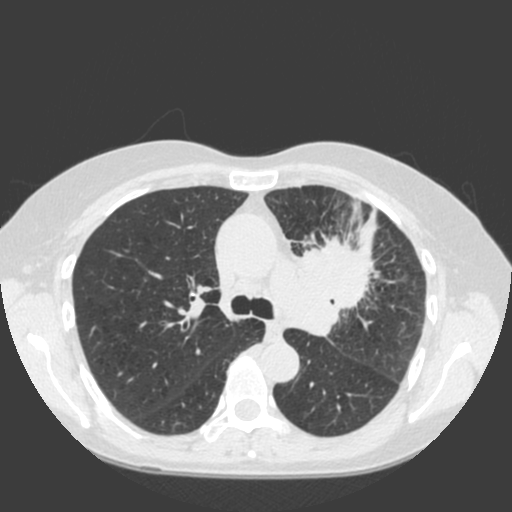
Low-dose screening chest CT, axial slice. Baseline annual screen. Lung window (W 1500 / L -600 HU). Standard (soft-tissue) reconstruction kernel (C). Slice 59 of 184 in the series. Female participant, aged 66 years at enrolment. Current smoker at enrolment.
Expert-annotated lung lesion, bounding box [x1, y1, x2, y2] px = [282, 224, 400, 330]. Reader record for this screening exam (exam-level; its link to the box is not recorded): non-calcified nodule or mass ≥4 mm, left upper lobe, 61 × 45 mm, spiculated (stellate) margins, soft tissue attenuation. Official screen result: positive, change unspecified: nodule(s) >= 4 mm or enlarging nodule(s), mass(es), or other non-specific abnormalities suspicious for lung cancer. Lung cancer was diagnosed 19 days after this screen: squamous cell carcinoma, keratinizing, NOS, left upper lobe, left hilum, mediastinum, left main stem bronchus, other location, poorly differentiated (G3), stage IIIB (AJCC 6th edition), 60 mm at pathology.